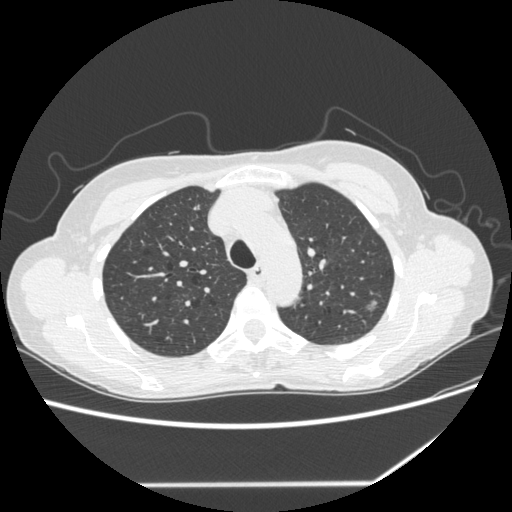
Low-dose screening chest CT, one axial slice. Position 198 of 255 along the scan axis. Reconstruction kernel STANDARD. 120 kVp. Lung window (W 1500 / L -600 HU). 512 × 512 image matrix.
Annotated regions visible in this slice (manually delineated by an expert):
- lesion 1 (tumor, upper lobe of left lung): box from (x=368, y=301) to (x=377, y=310) px